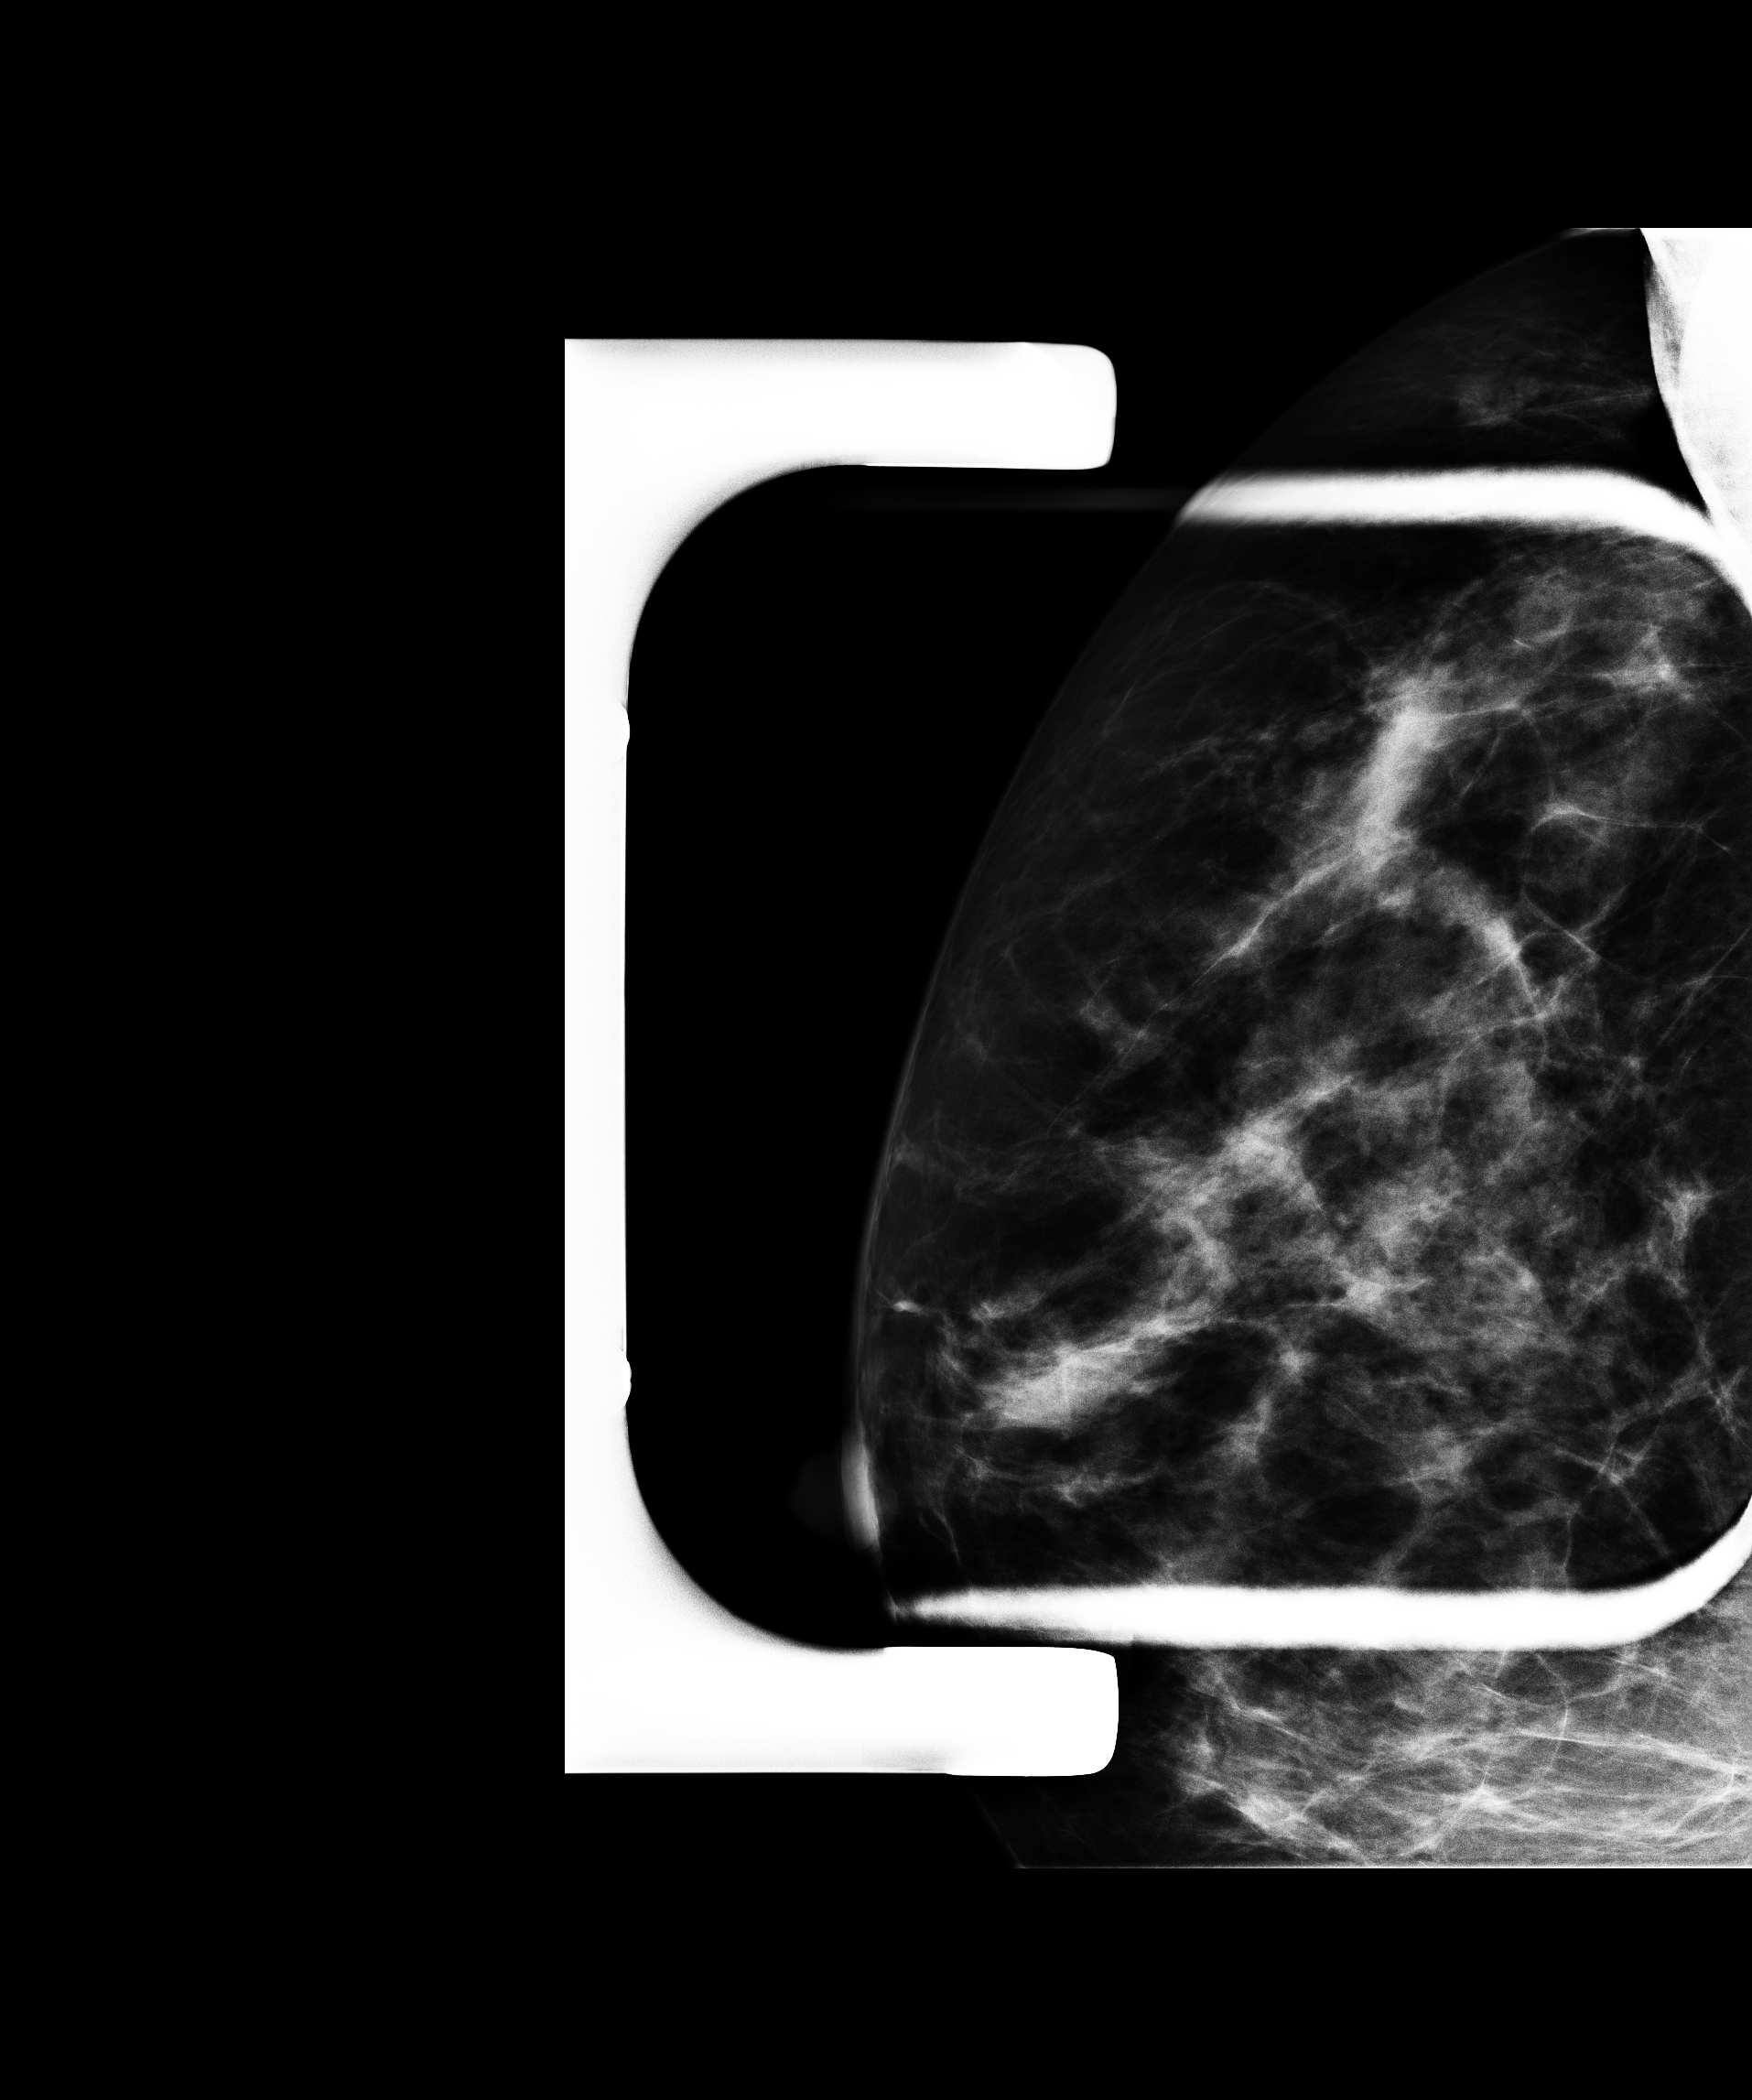
Additional (diagnostic) view.
Image type: full-field digital mammogram. Breast: right. Projection: CC view, spot compression.